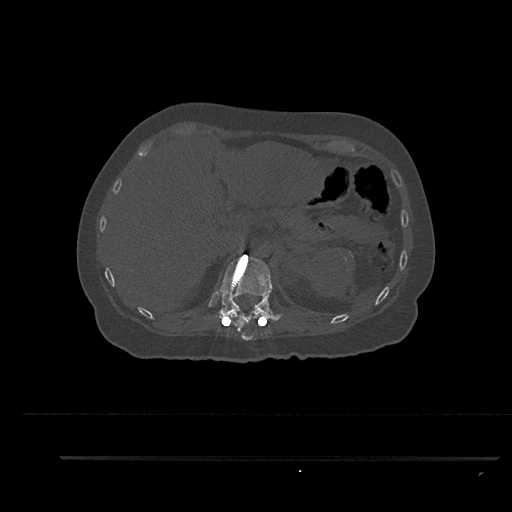
CT including the spine, one axial slice. Position 283 of 797 along the scan axis. Reconstruction kernel Br40s/3. 120 kVp. Bone window (W 1800 / L 400 HU). 0.5 mm slice thickness. 512 × 512 image matrix. Female patient, age 44 years. Case-level facts recorded for this patient, not image findings: primary cancer: renal; vertebrae with lytic lesions (as recorded): L1.
Annotated regions visible in this slice (semi-automatically segmented with operator editing):
- T11 vertebra: bounding box (x1, y1, x2, y2) in pixels: (232, 310, 261, 340)
- T12 vertebra: (219, 246, 282, 322)